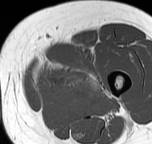
MRI of an extremity soft-tissue mass, one axial slice; position 16 of 57 along the scan axis; MR volume resampled by the dataset authors to the PET/CT grid (not the native acquisition matrix); 152 × 144 image matrix. Female patient. From the clinical record (not read from this slice): histological type: pleiomorphic leiomyosarcoma; grade: intermediate; site of the primary tumour: left thigh.
Structures marked on this image (expert contour drawn on MRI and transferred to this co-registered scan by the dataset authors):
- gross tumour volume including surrounding oedema: bounding box <32,56,101,98> (left, top, right, bottom; pixels)